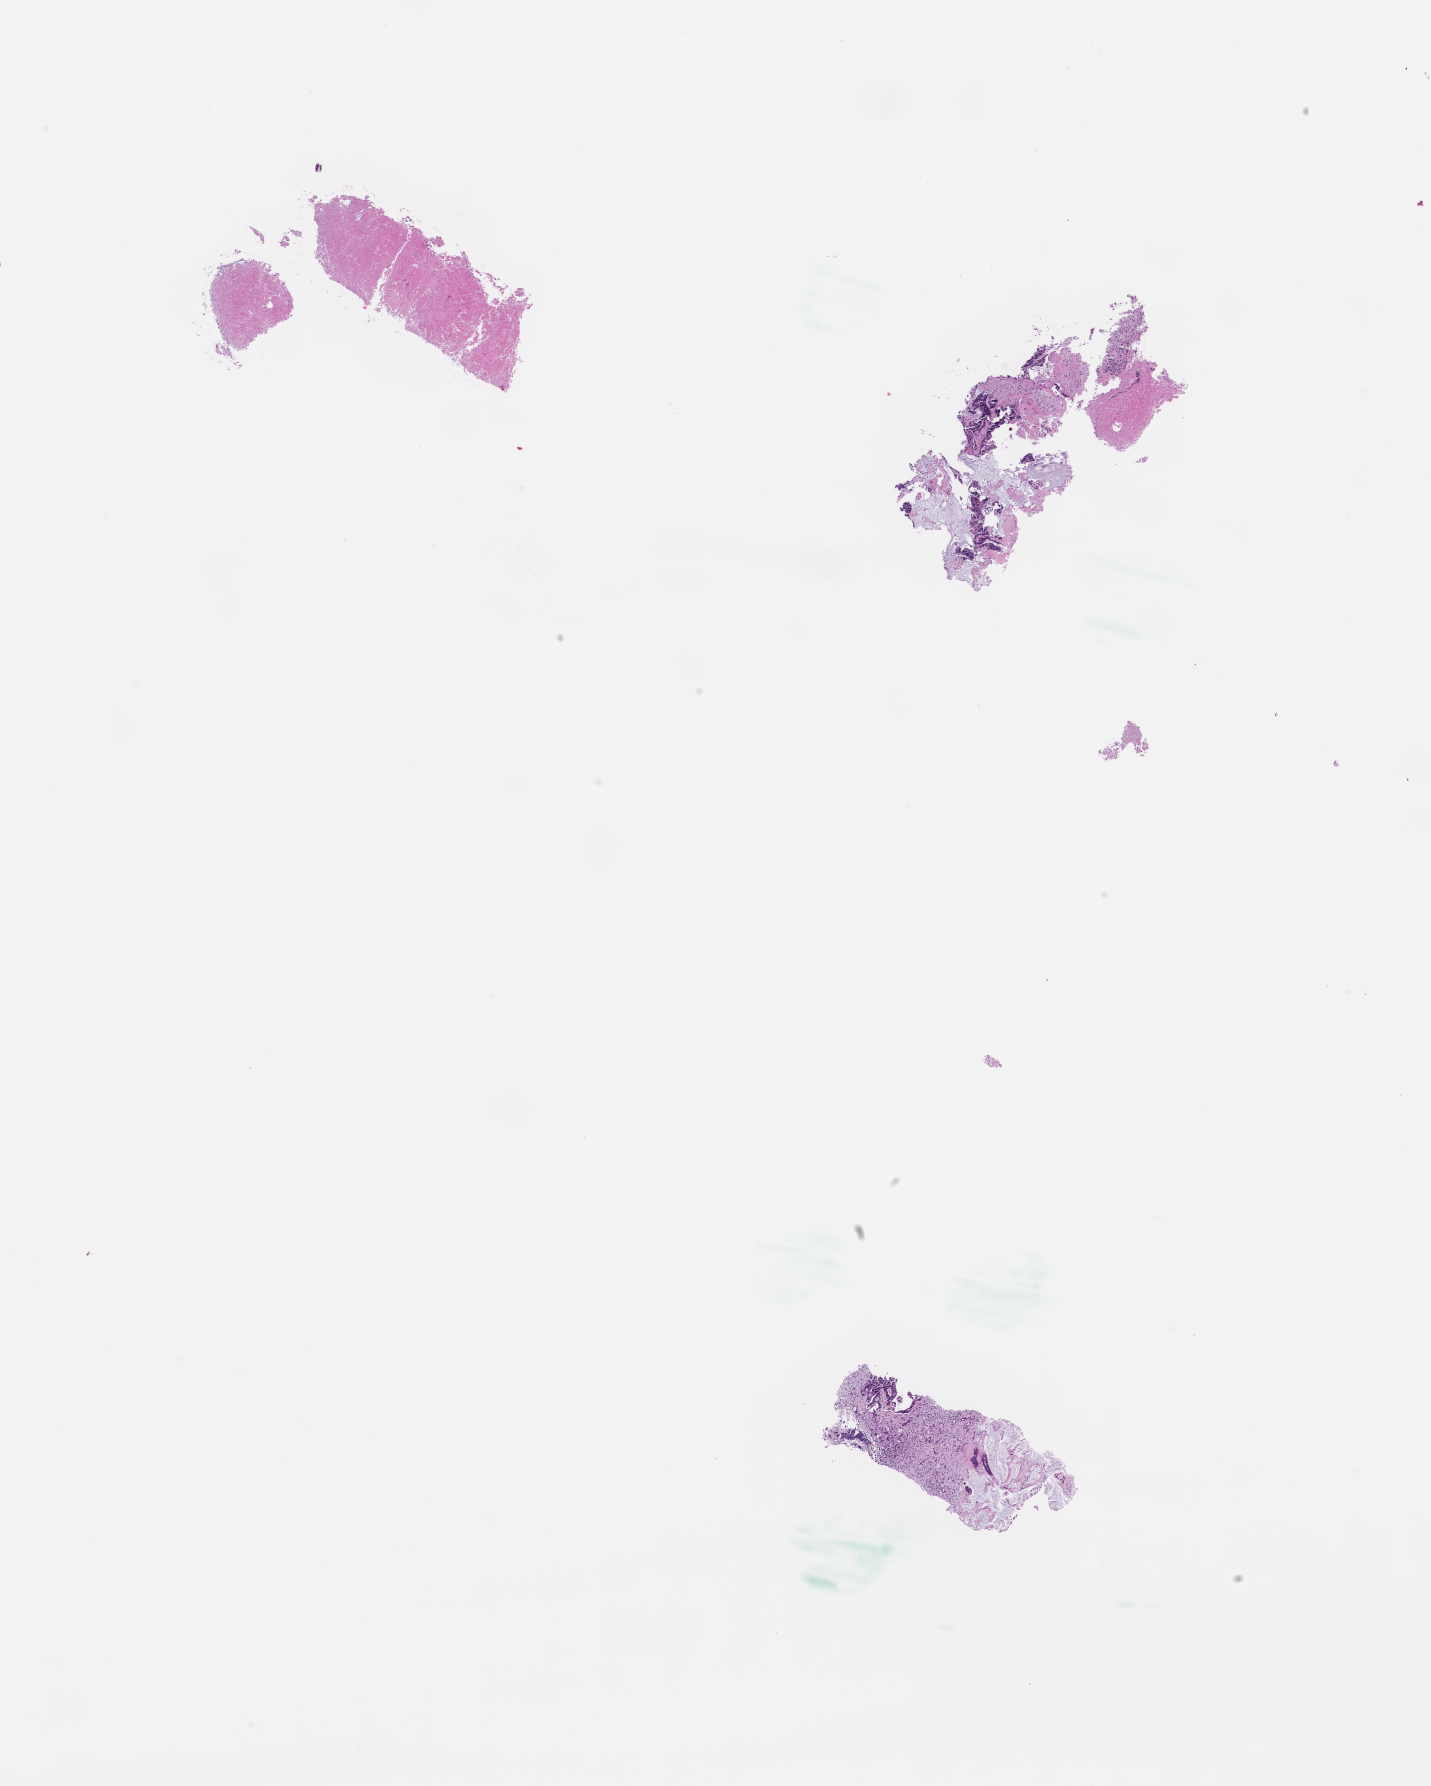
Whole-slide image, hematoxylin and eosin (H&E) stain — whole scanned area (about 11.6 x 14.4 mm) shown as a low-resolution overview; formalin-fixed, paraffin-embedded (FFPE) tissue; specimen time point: collected at disease progression. Patient: female.
This section: metastasis (sampled organ not recorded). Patient diagnosis (primary): Colorectal Carcinoma.